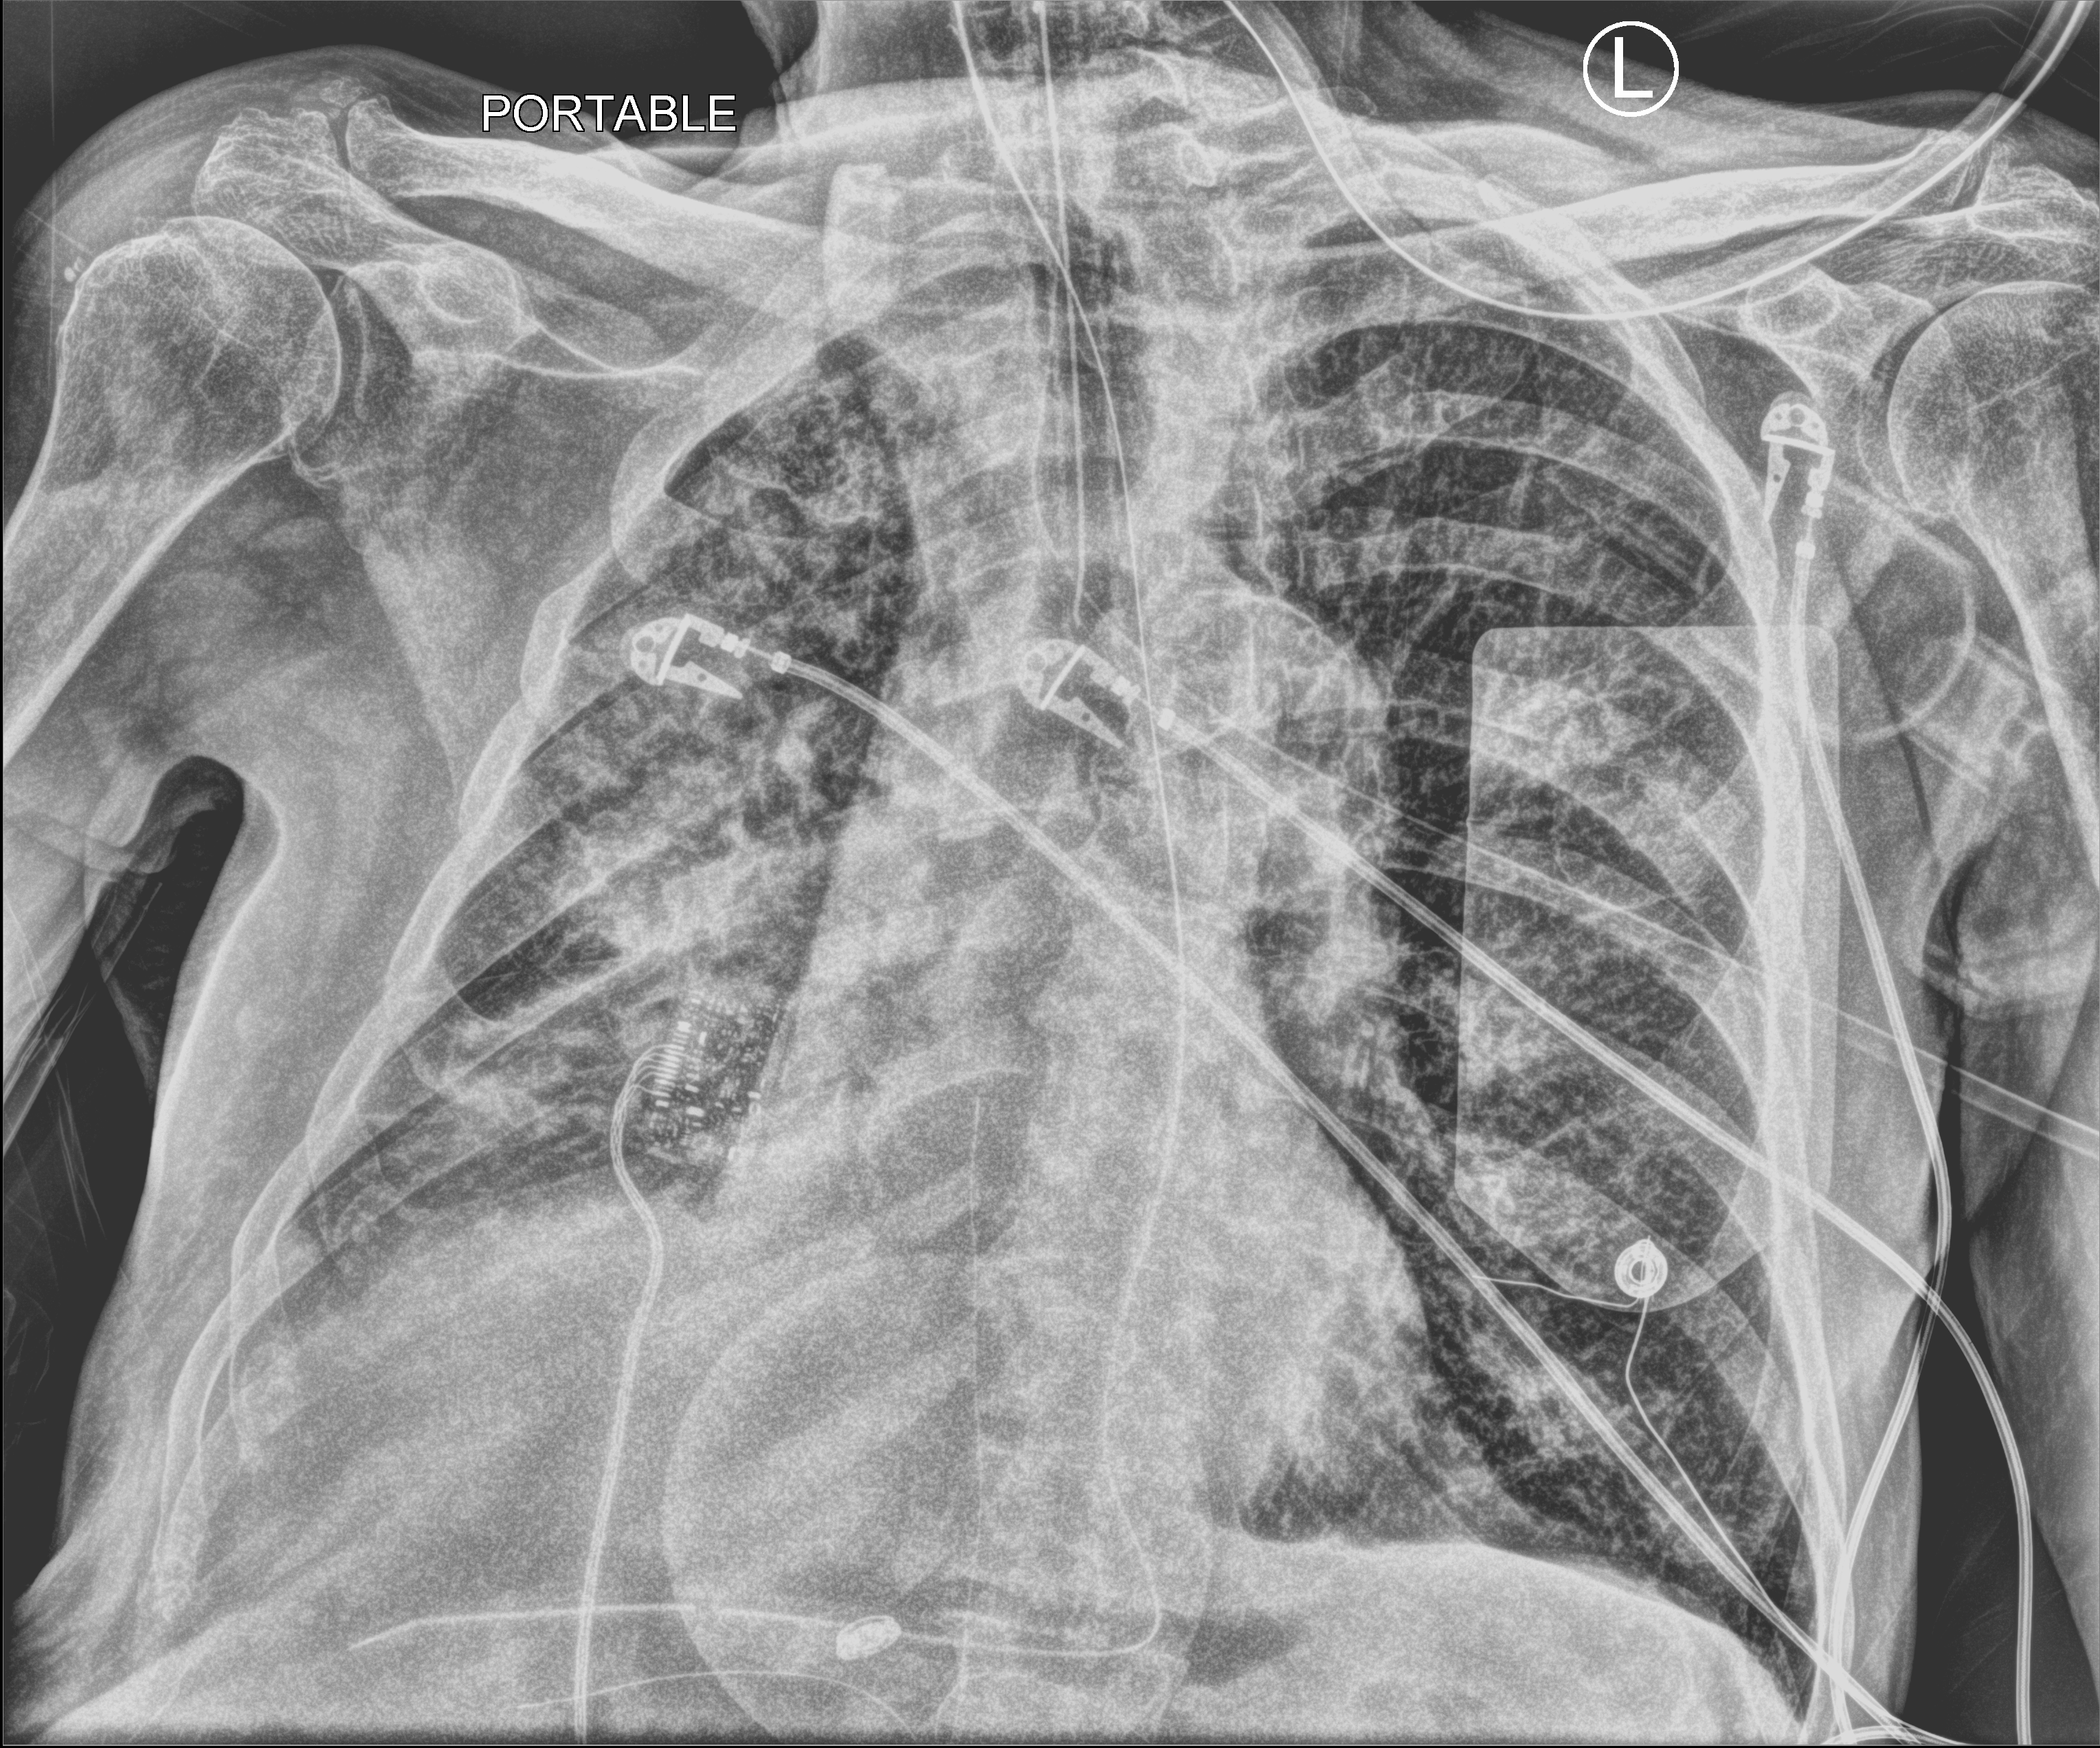
Chest X-ray (portable), anteroposterior (AP) projection. Male patient hospitalised with COVID-19, age 75–90 years.
Hospital-stay facts (about this admission, not read from this image; timing relative to this image not recorded):
- diabetes (admission record): yes